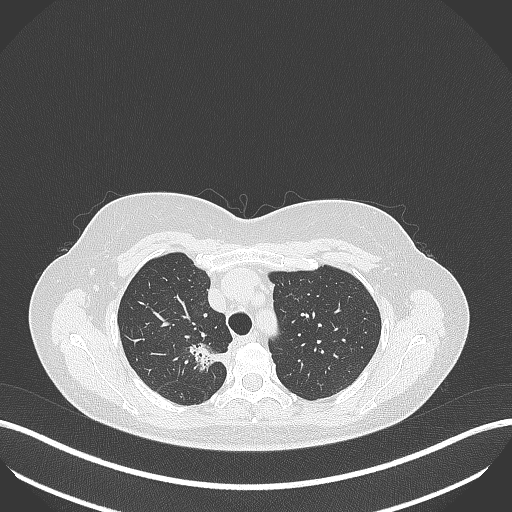
Chest CT, one axial slice. Position 302 of 386 along the scan axis. Reconstruction kernel B70f. 120 kVp. Lung window (W 1500 / L -600 HU). 512 × 512 image matrix, field of view 400 × 400 mm. Female patient, age 65 years. From the clinical record (not read from this slice): clinical TNM (as recorded): T1b N0 M0.
Outlined on this slice (bounding box drawn by a radiologist):
- lung tumour (recorded histology: adenocarcinoma): bounding box <186,337,229,376> (left, top, right, bottom; pixels)